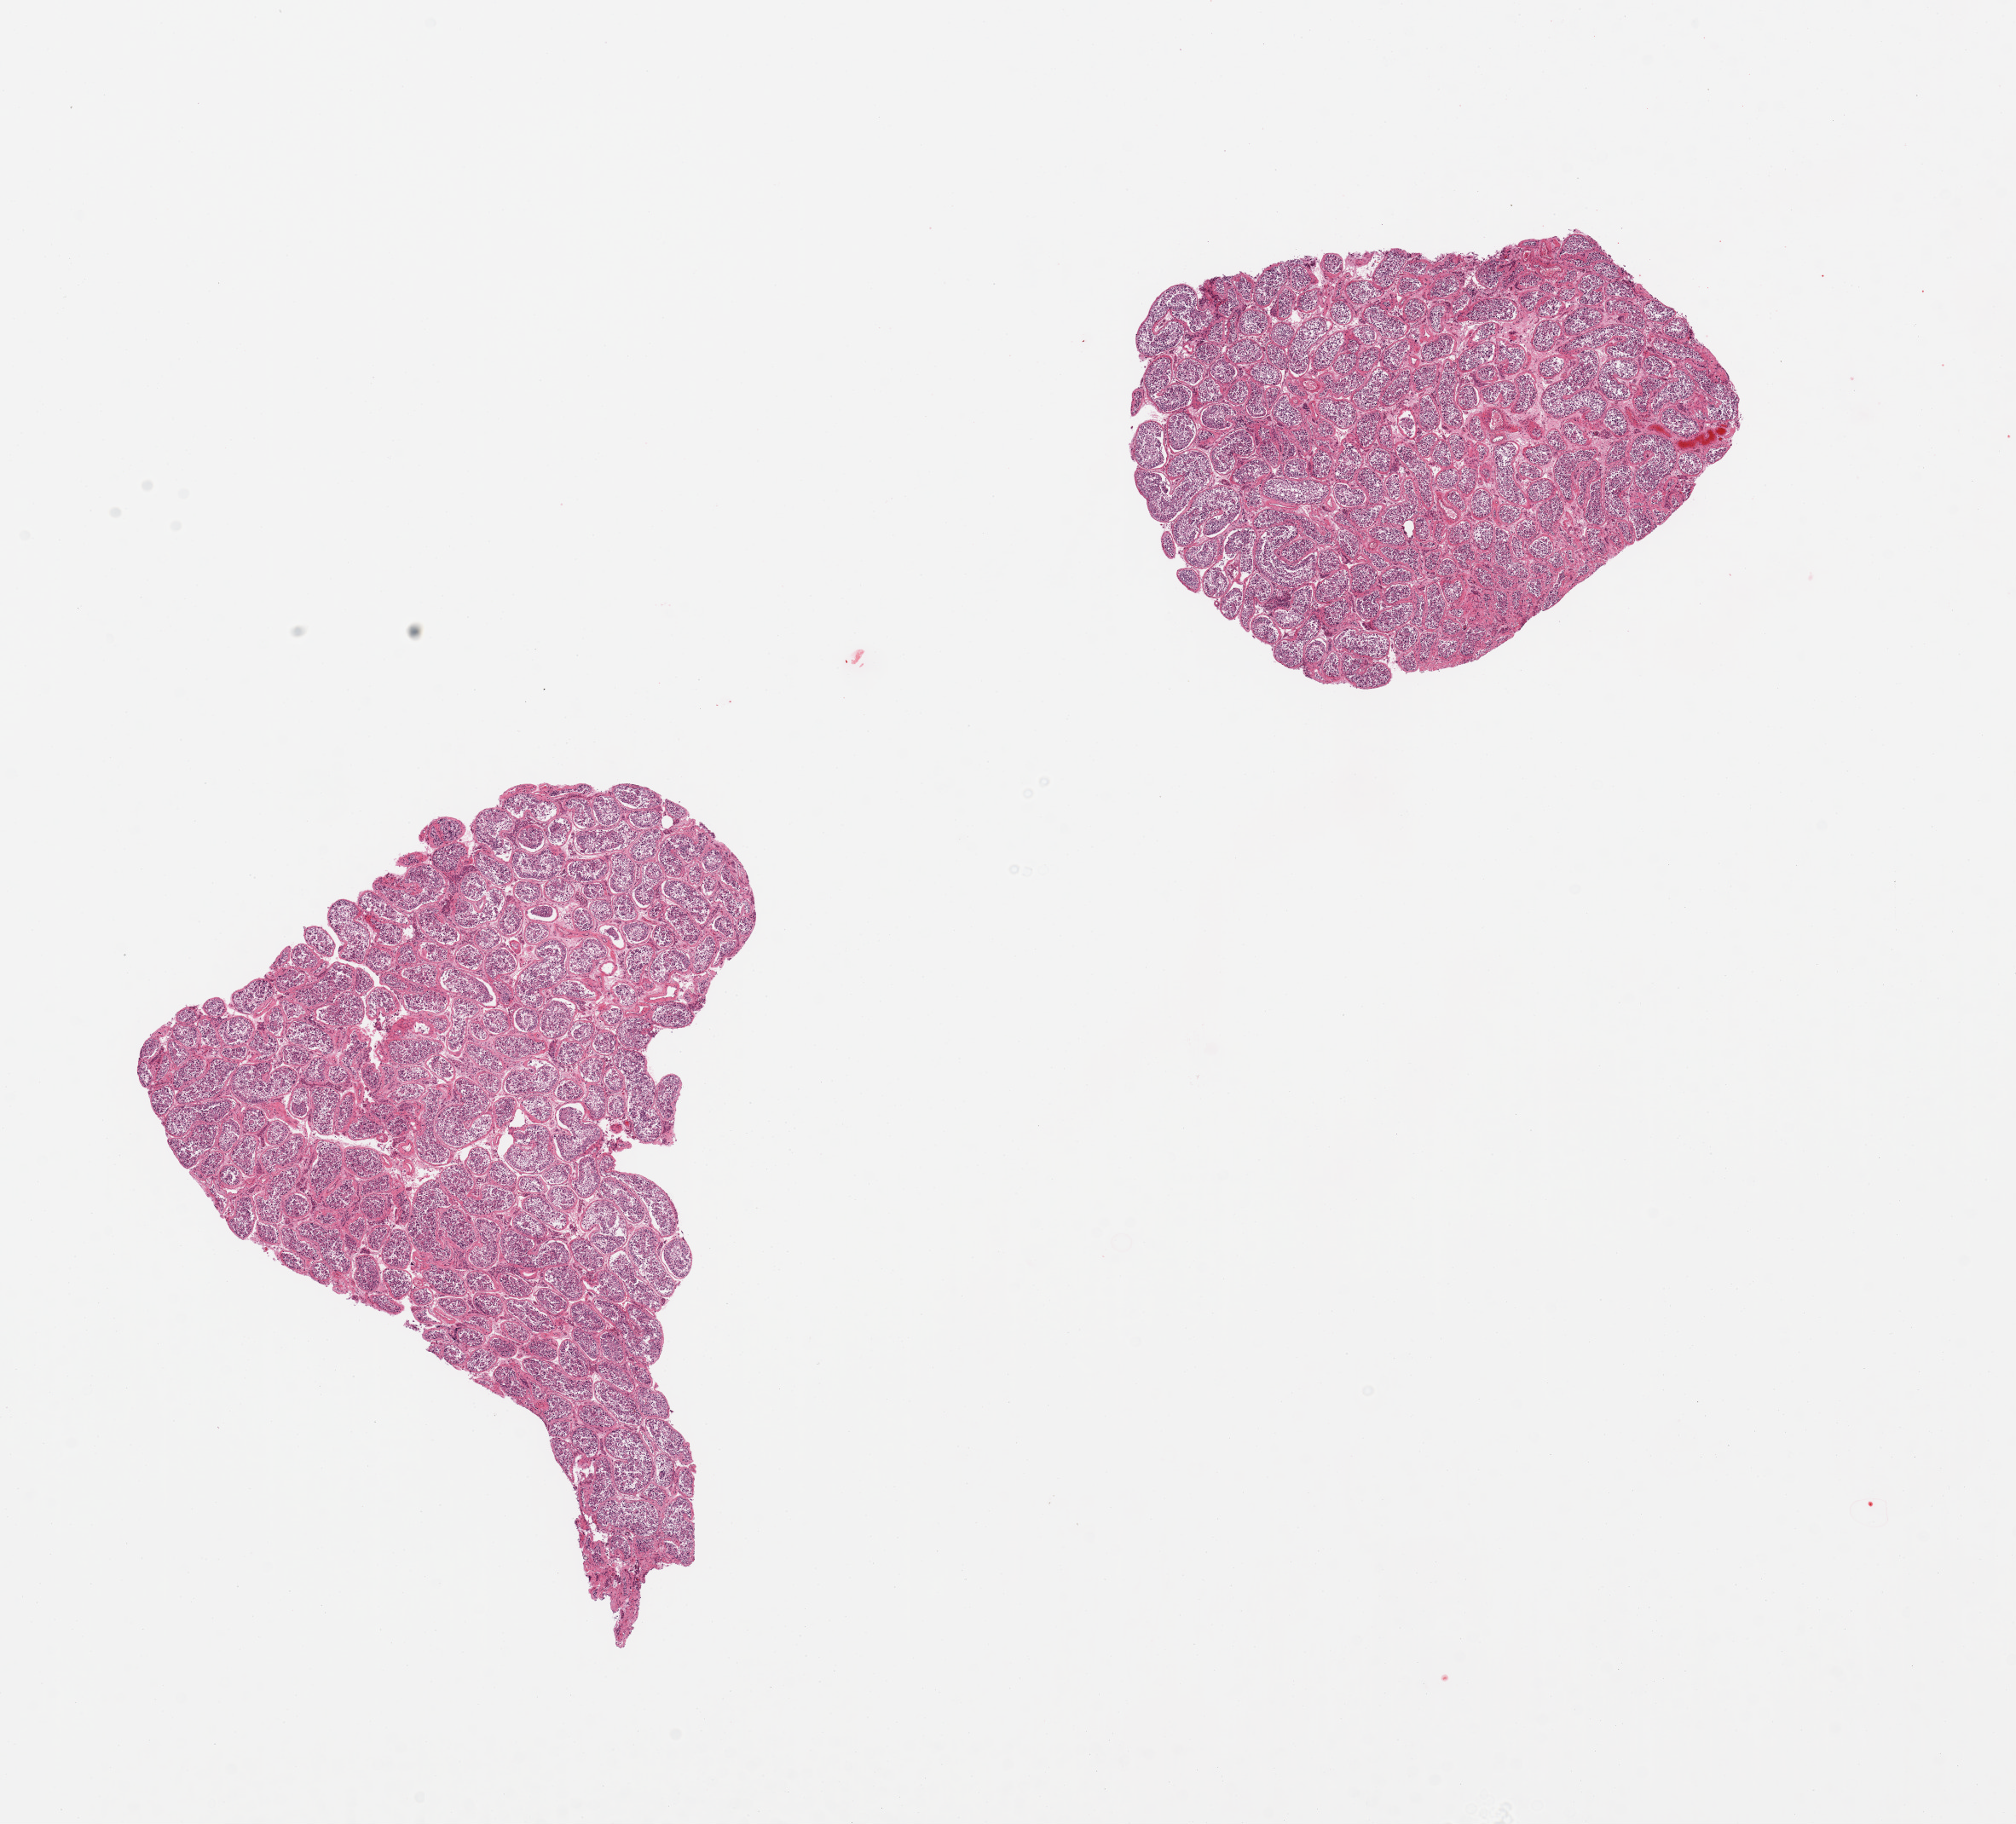
Haematoxylin and eosin whole-slide image — low-resolution overview of the scanned area, about 18.7 x 16.9 mm (slide scanned at 20x), PAXgene-fixed, paraffin-embedded tissue, sampled site (target tissue): testis, donor tissue sample.
* reviewer comment on this tissue sample: 2 pieces, spermatogenesis is present